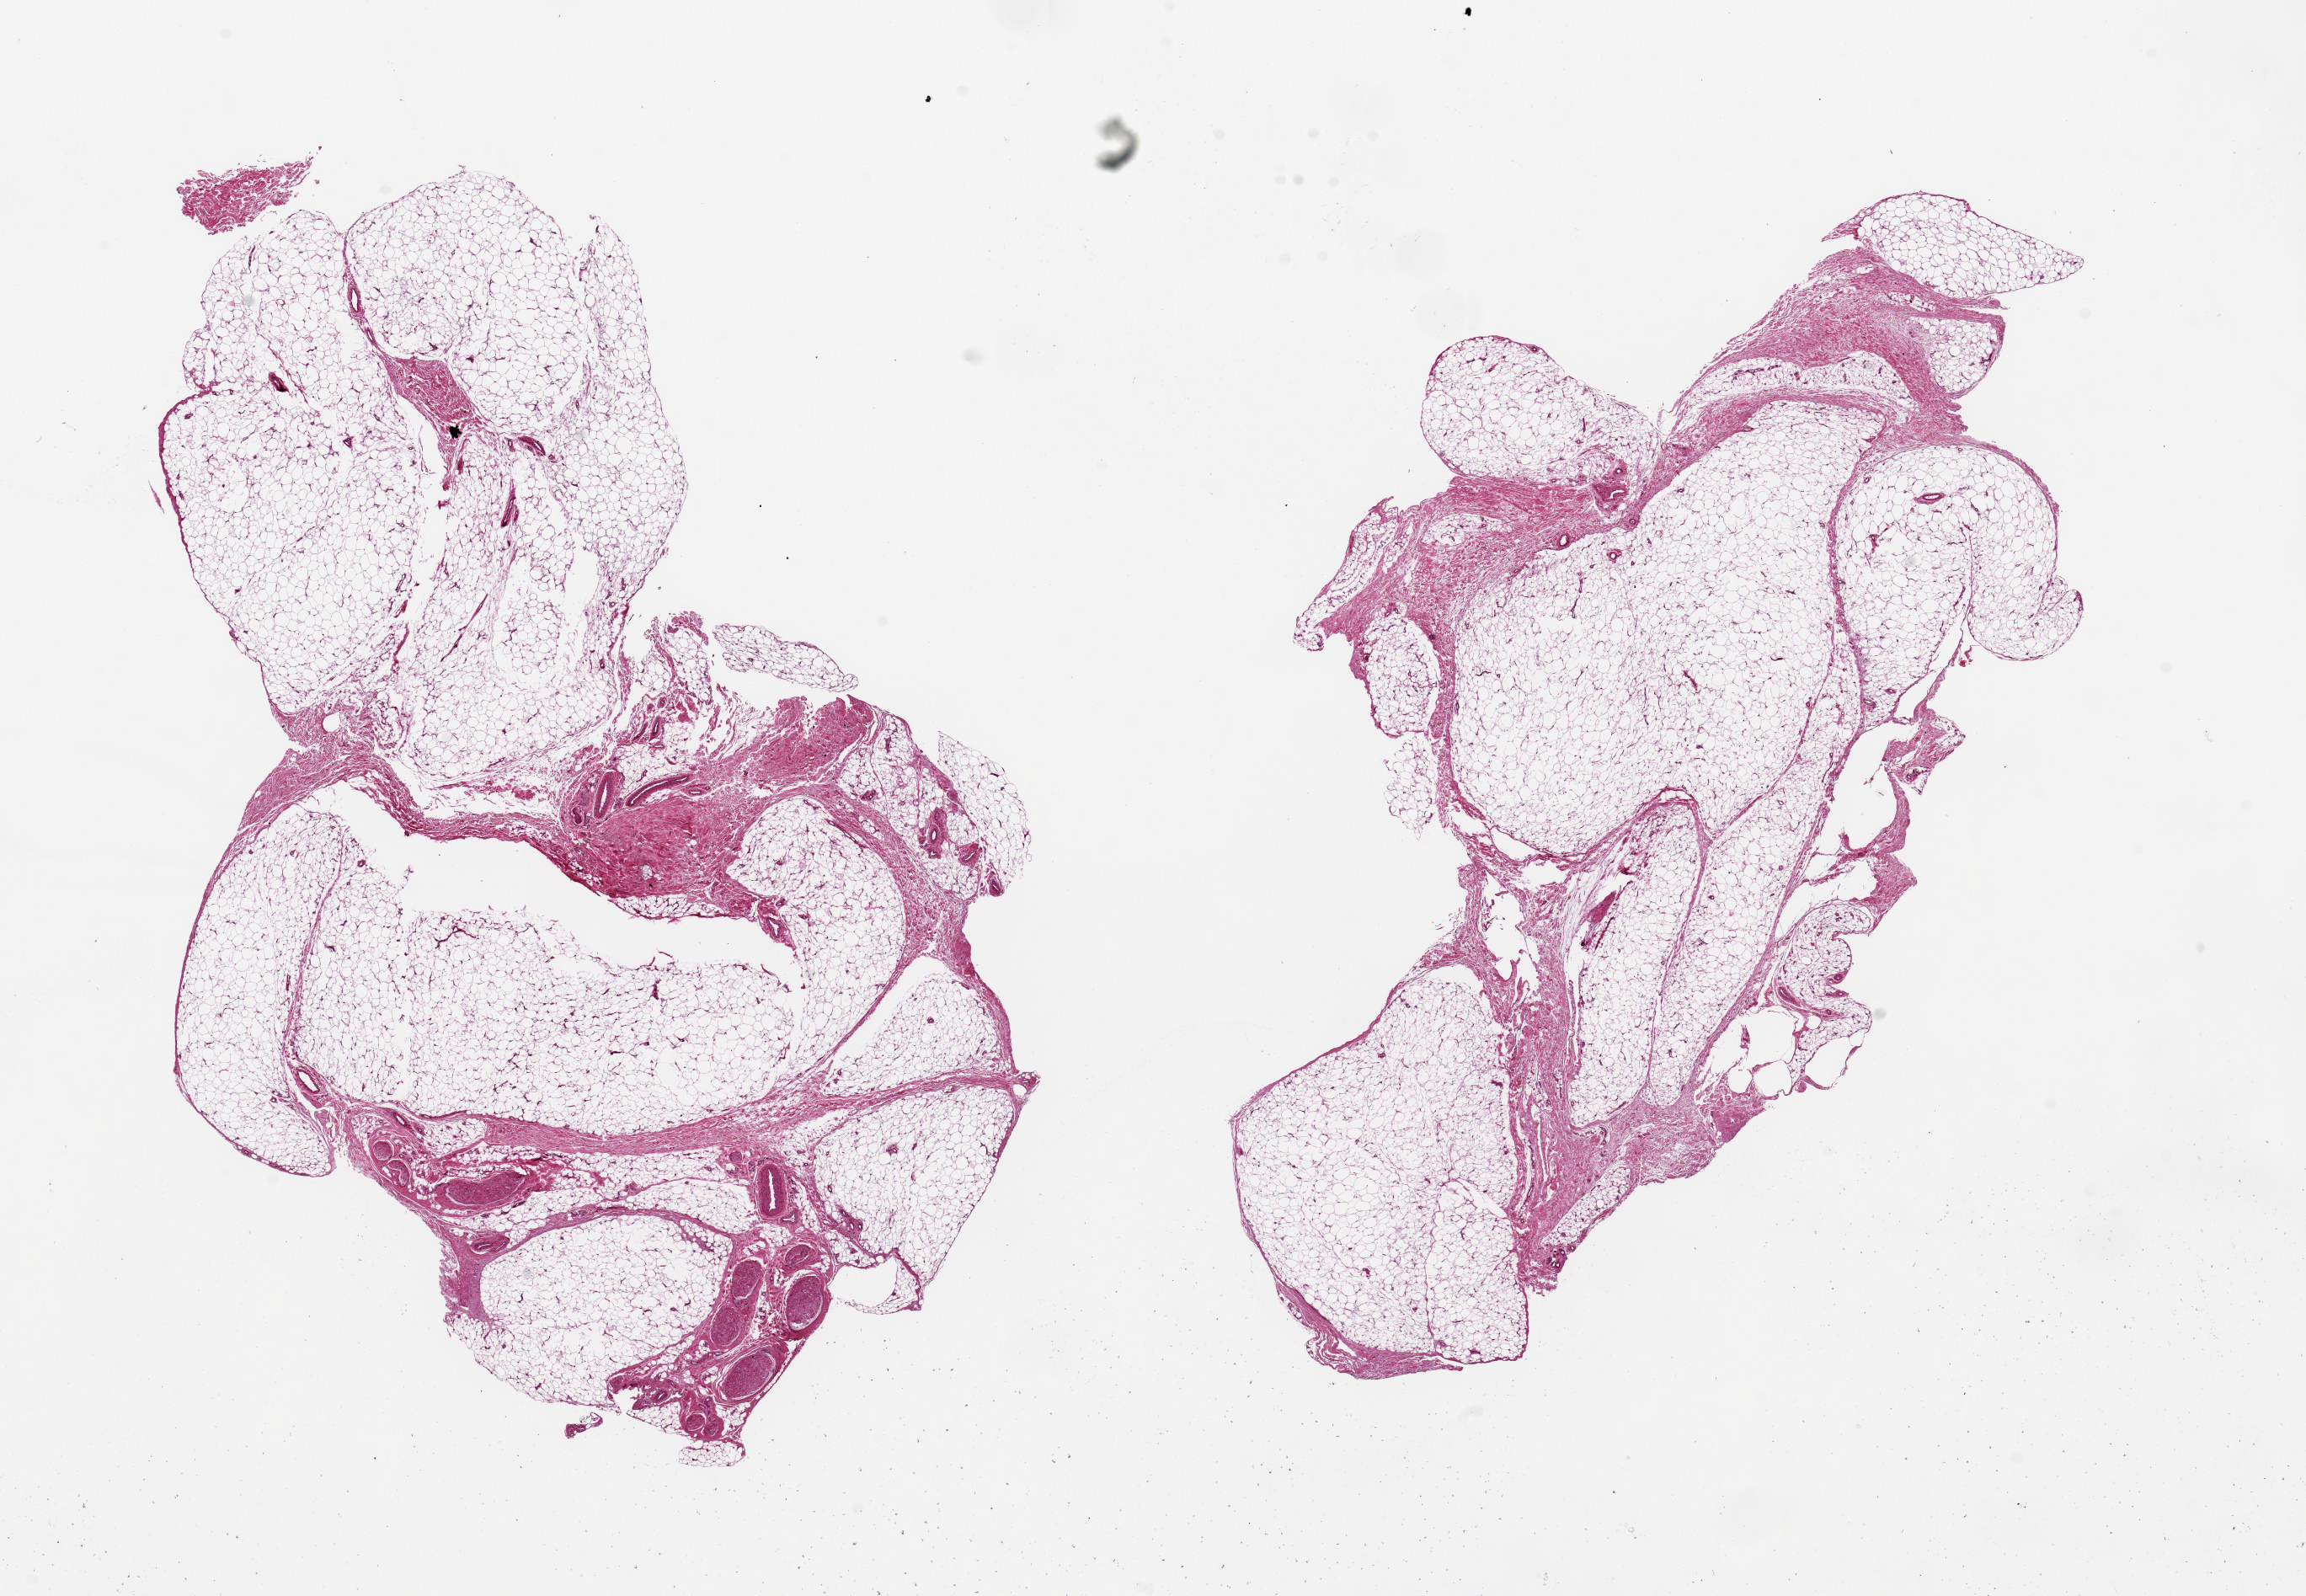
Digitized H&E-stained section — a low-resolution overview of the entire scanned area, about 21.7 x 15.0 mm (acquisition: 20x scan). PAXgene-fixed, paraffin-embedded tissue. Section of adipose tissue (target tissue). Tissue donor sample. Male donor.
* review note (as recorded): 2 pieces ~12x5mm; Contaminant' nerve vascular tissue in one up to ~2x1mm